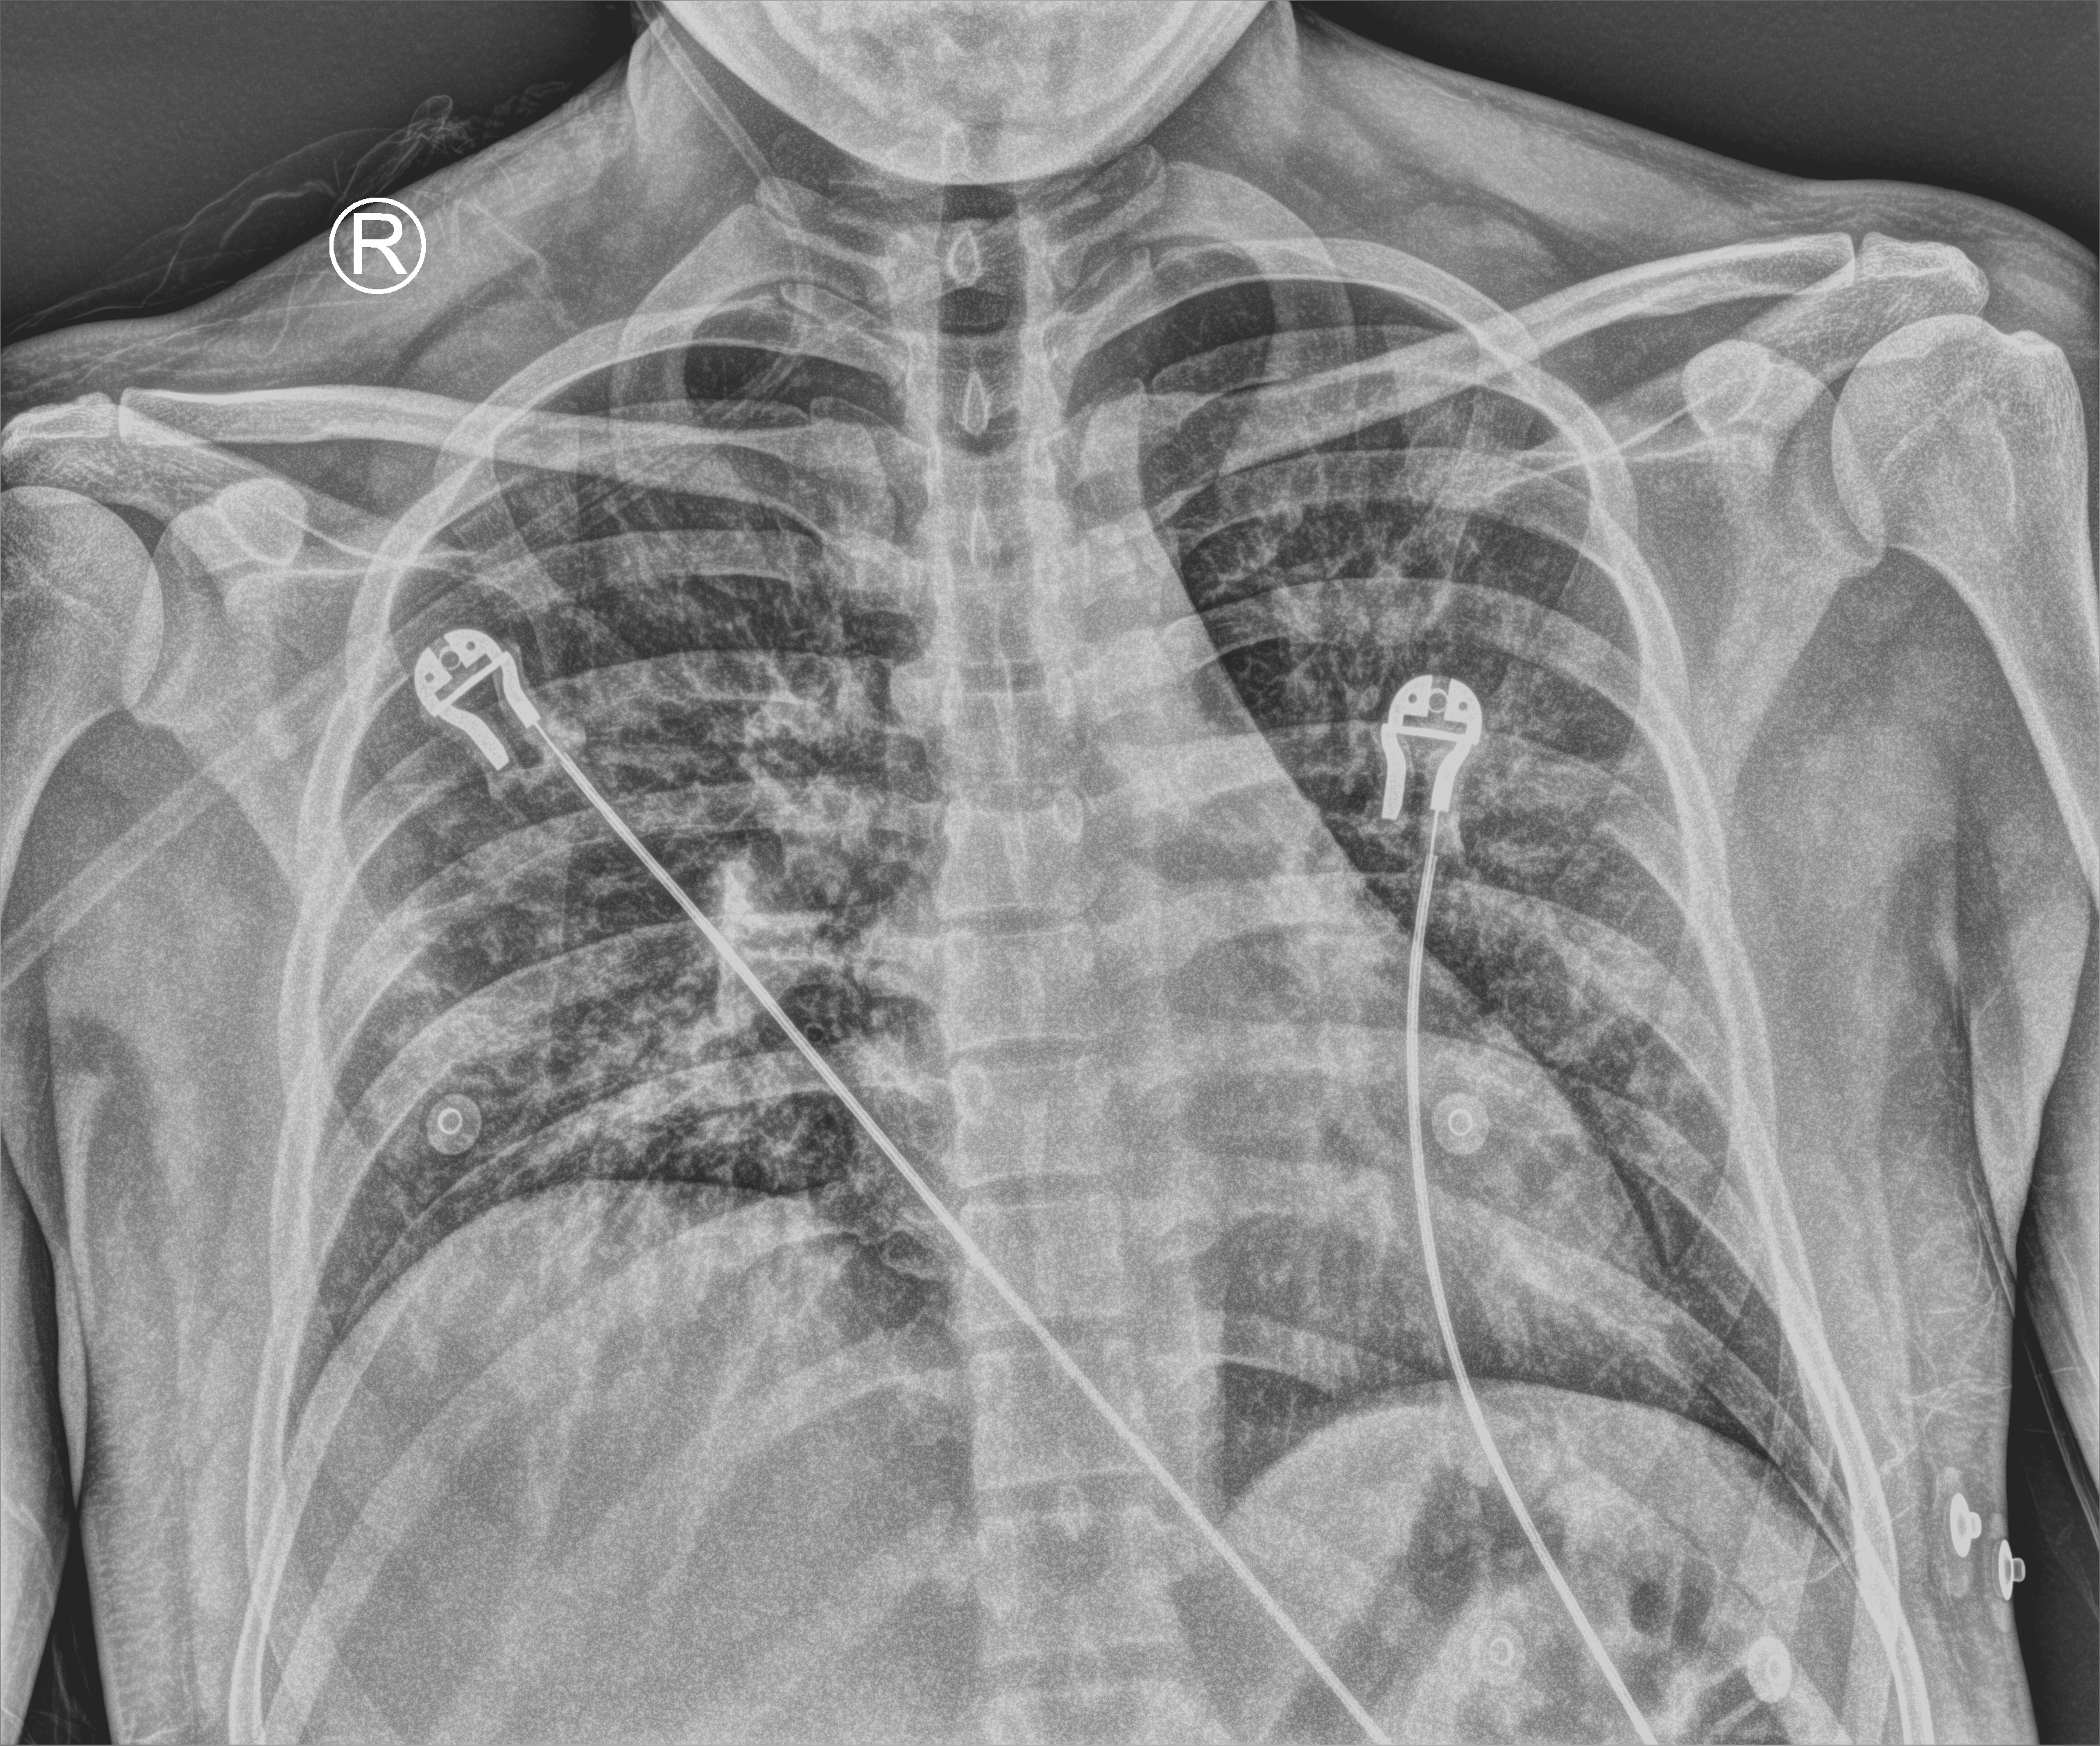
Chest X-ray (portable). Male patient hospitalised with COVID-19, age 18–59 years.
Admission-level facts for this patient (not findings on this image; timing relative to this image not recorded): mechanically ventilated during this hospital stay: yes; admitted to intensive care during this hospital stay: no; diabetes (admission record): no.